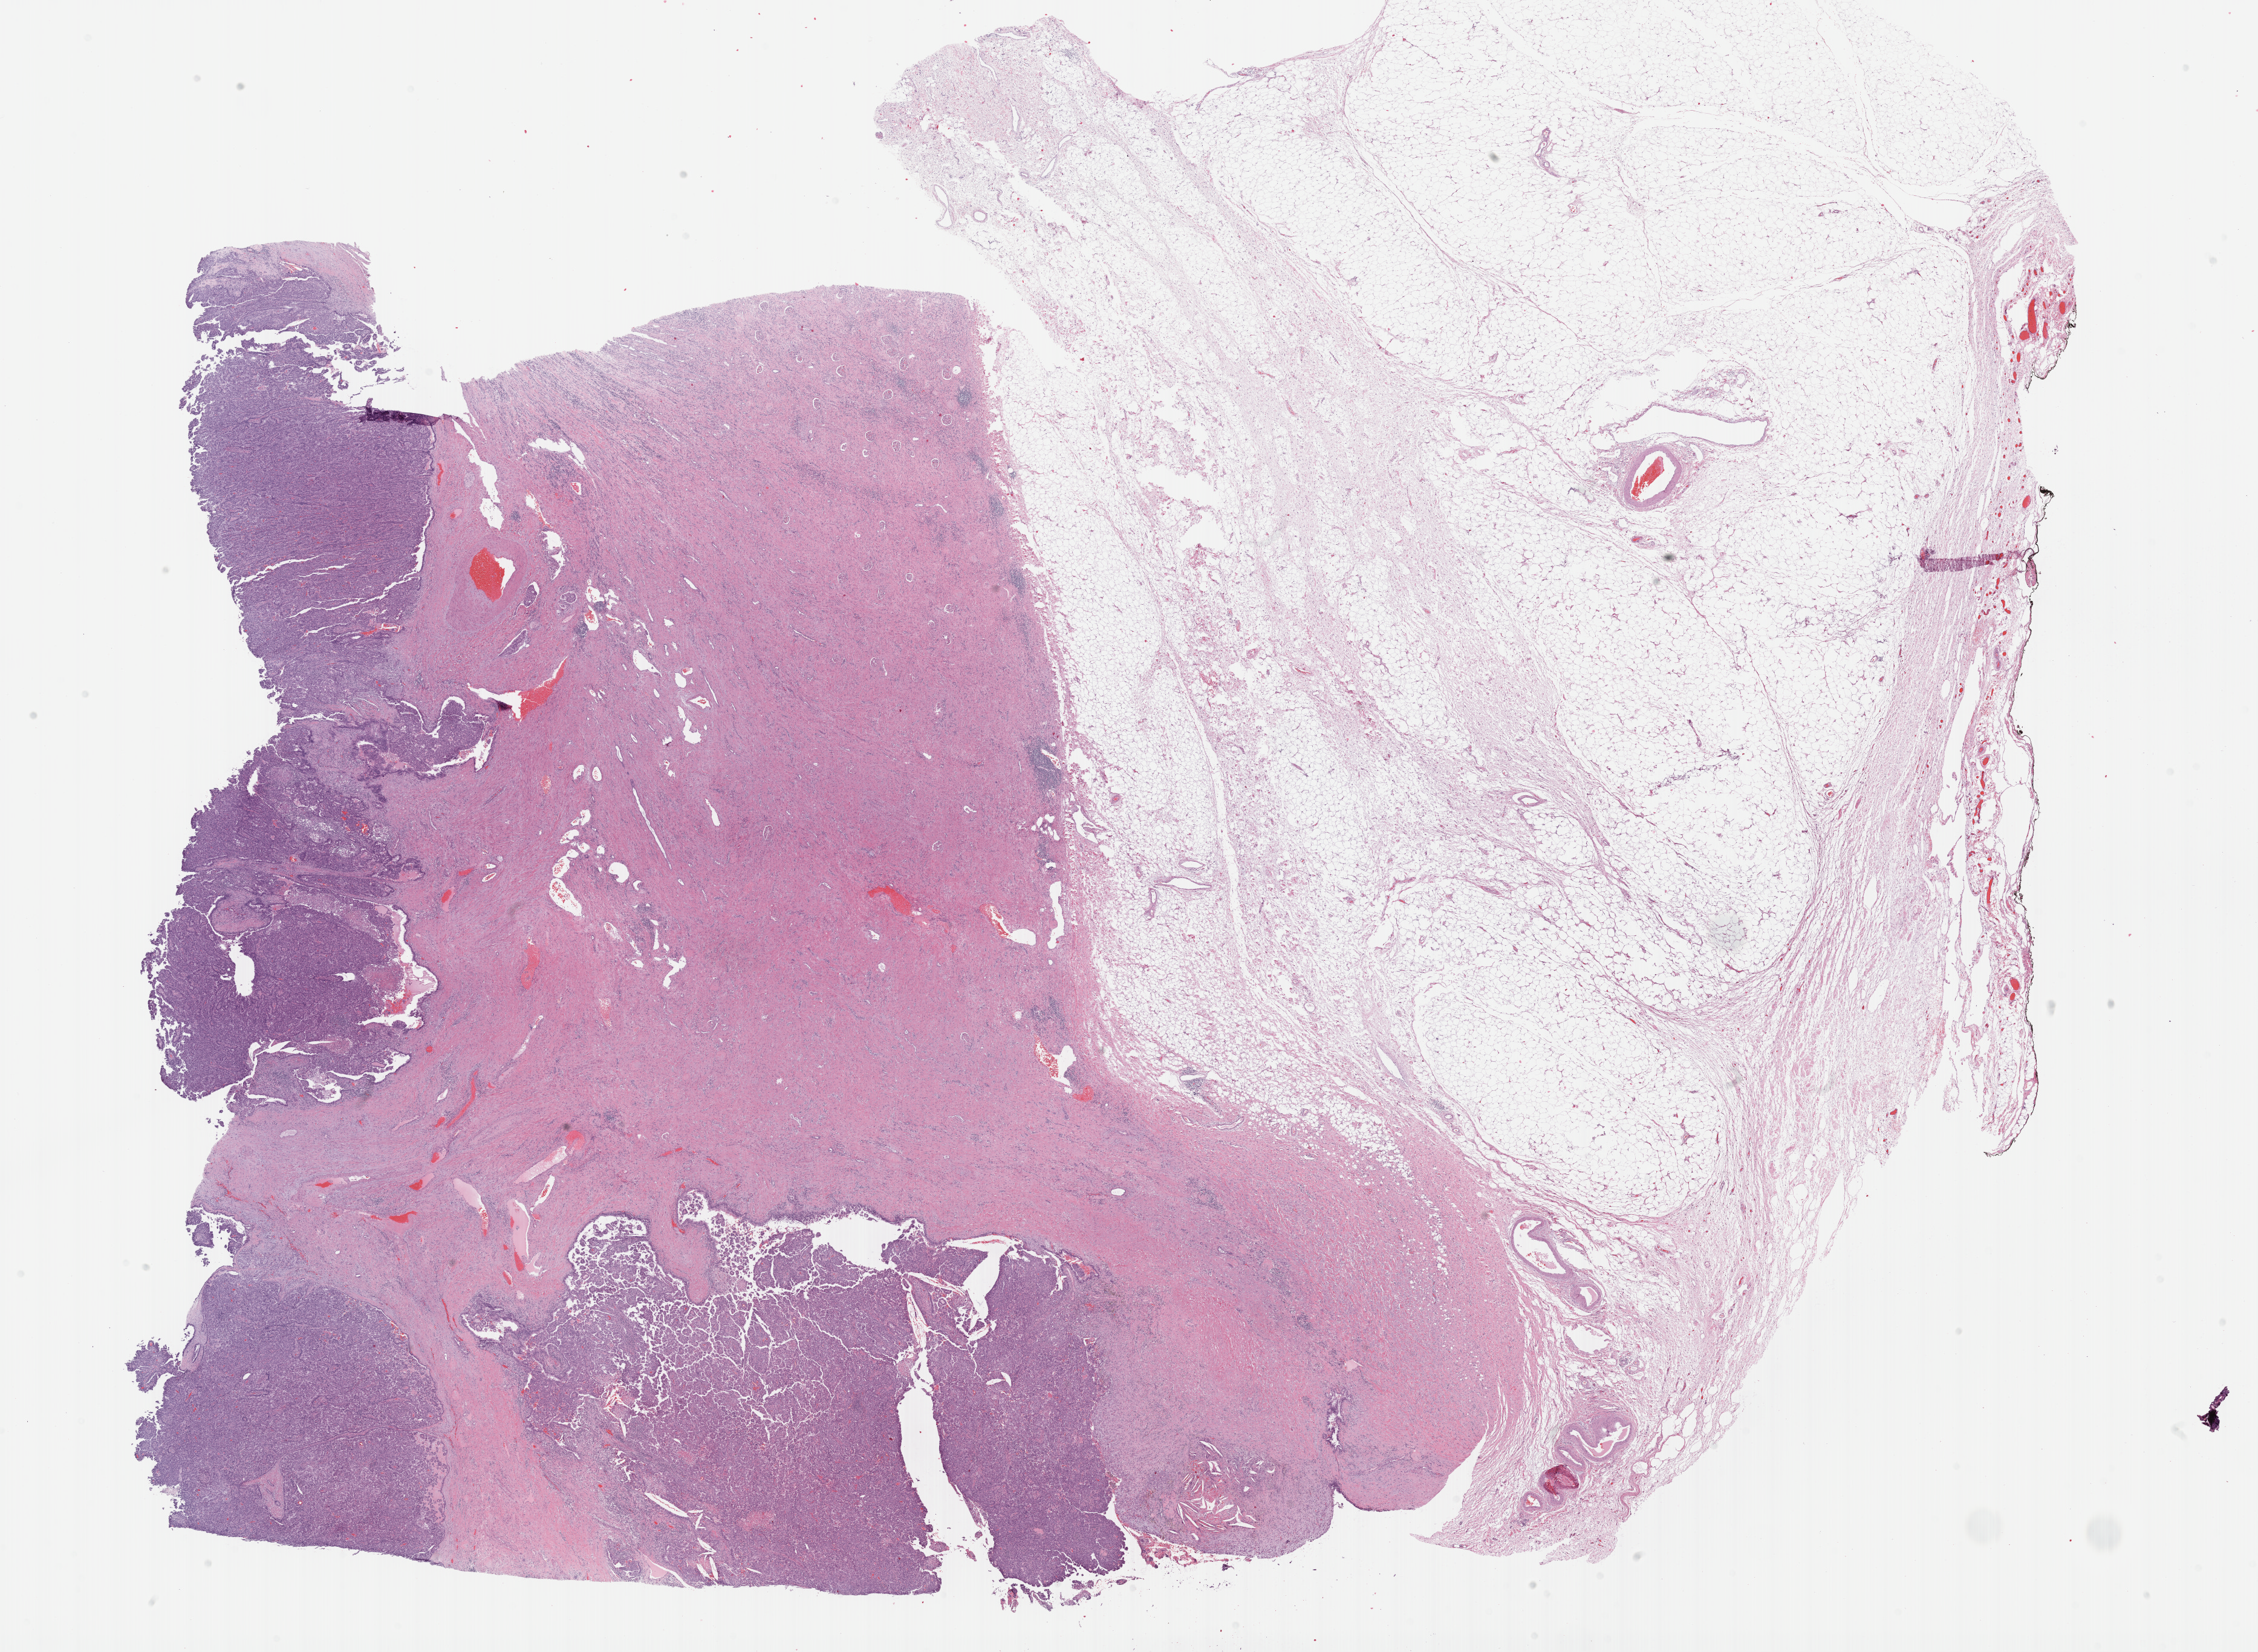
H&E-stained whole-slide image — low-resolution overview of the scanned area, about 30.2 x 22.1 mm. Formalin-fixed paraffin-embedded (FFPE) diagnostic section. Primary tumour sample from the kidney. Male, age 71 years at initial diagnosis.
Diagnosis: Papillary adenocarcinoma, NOS.